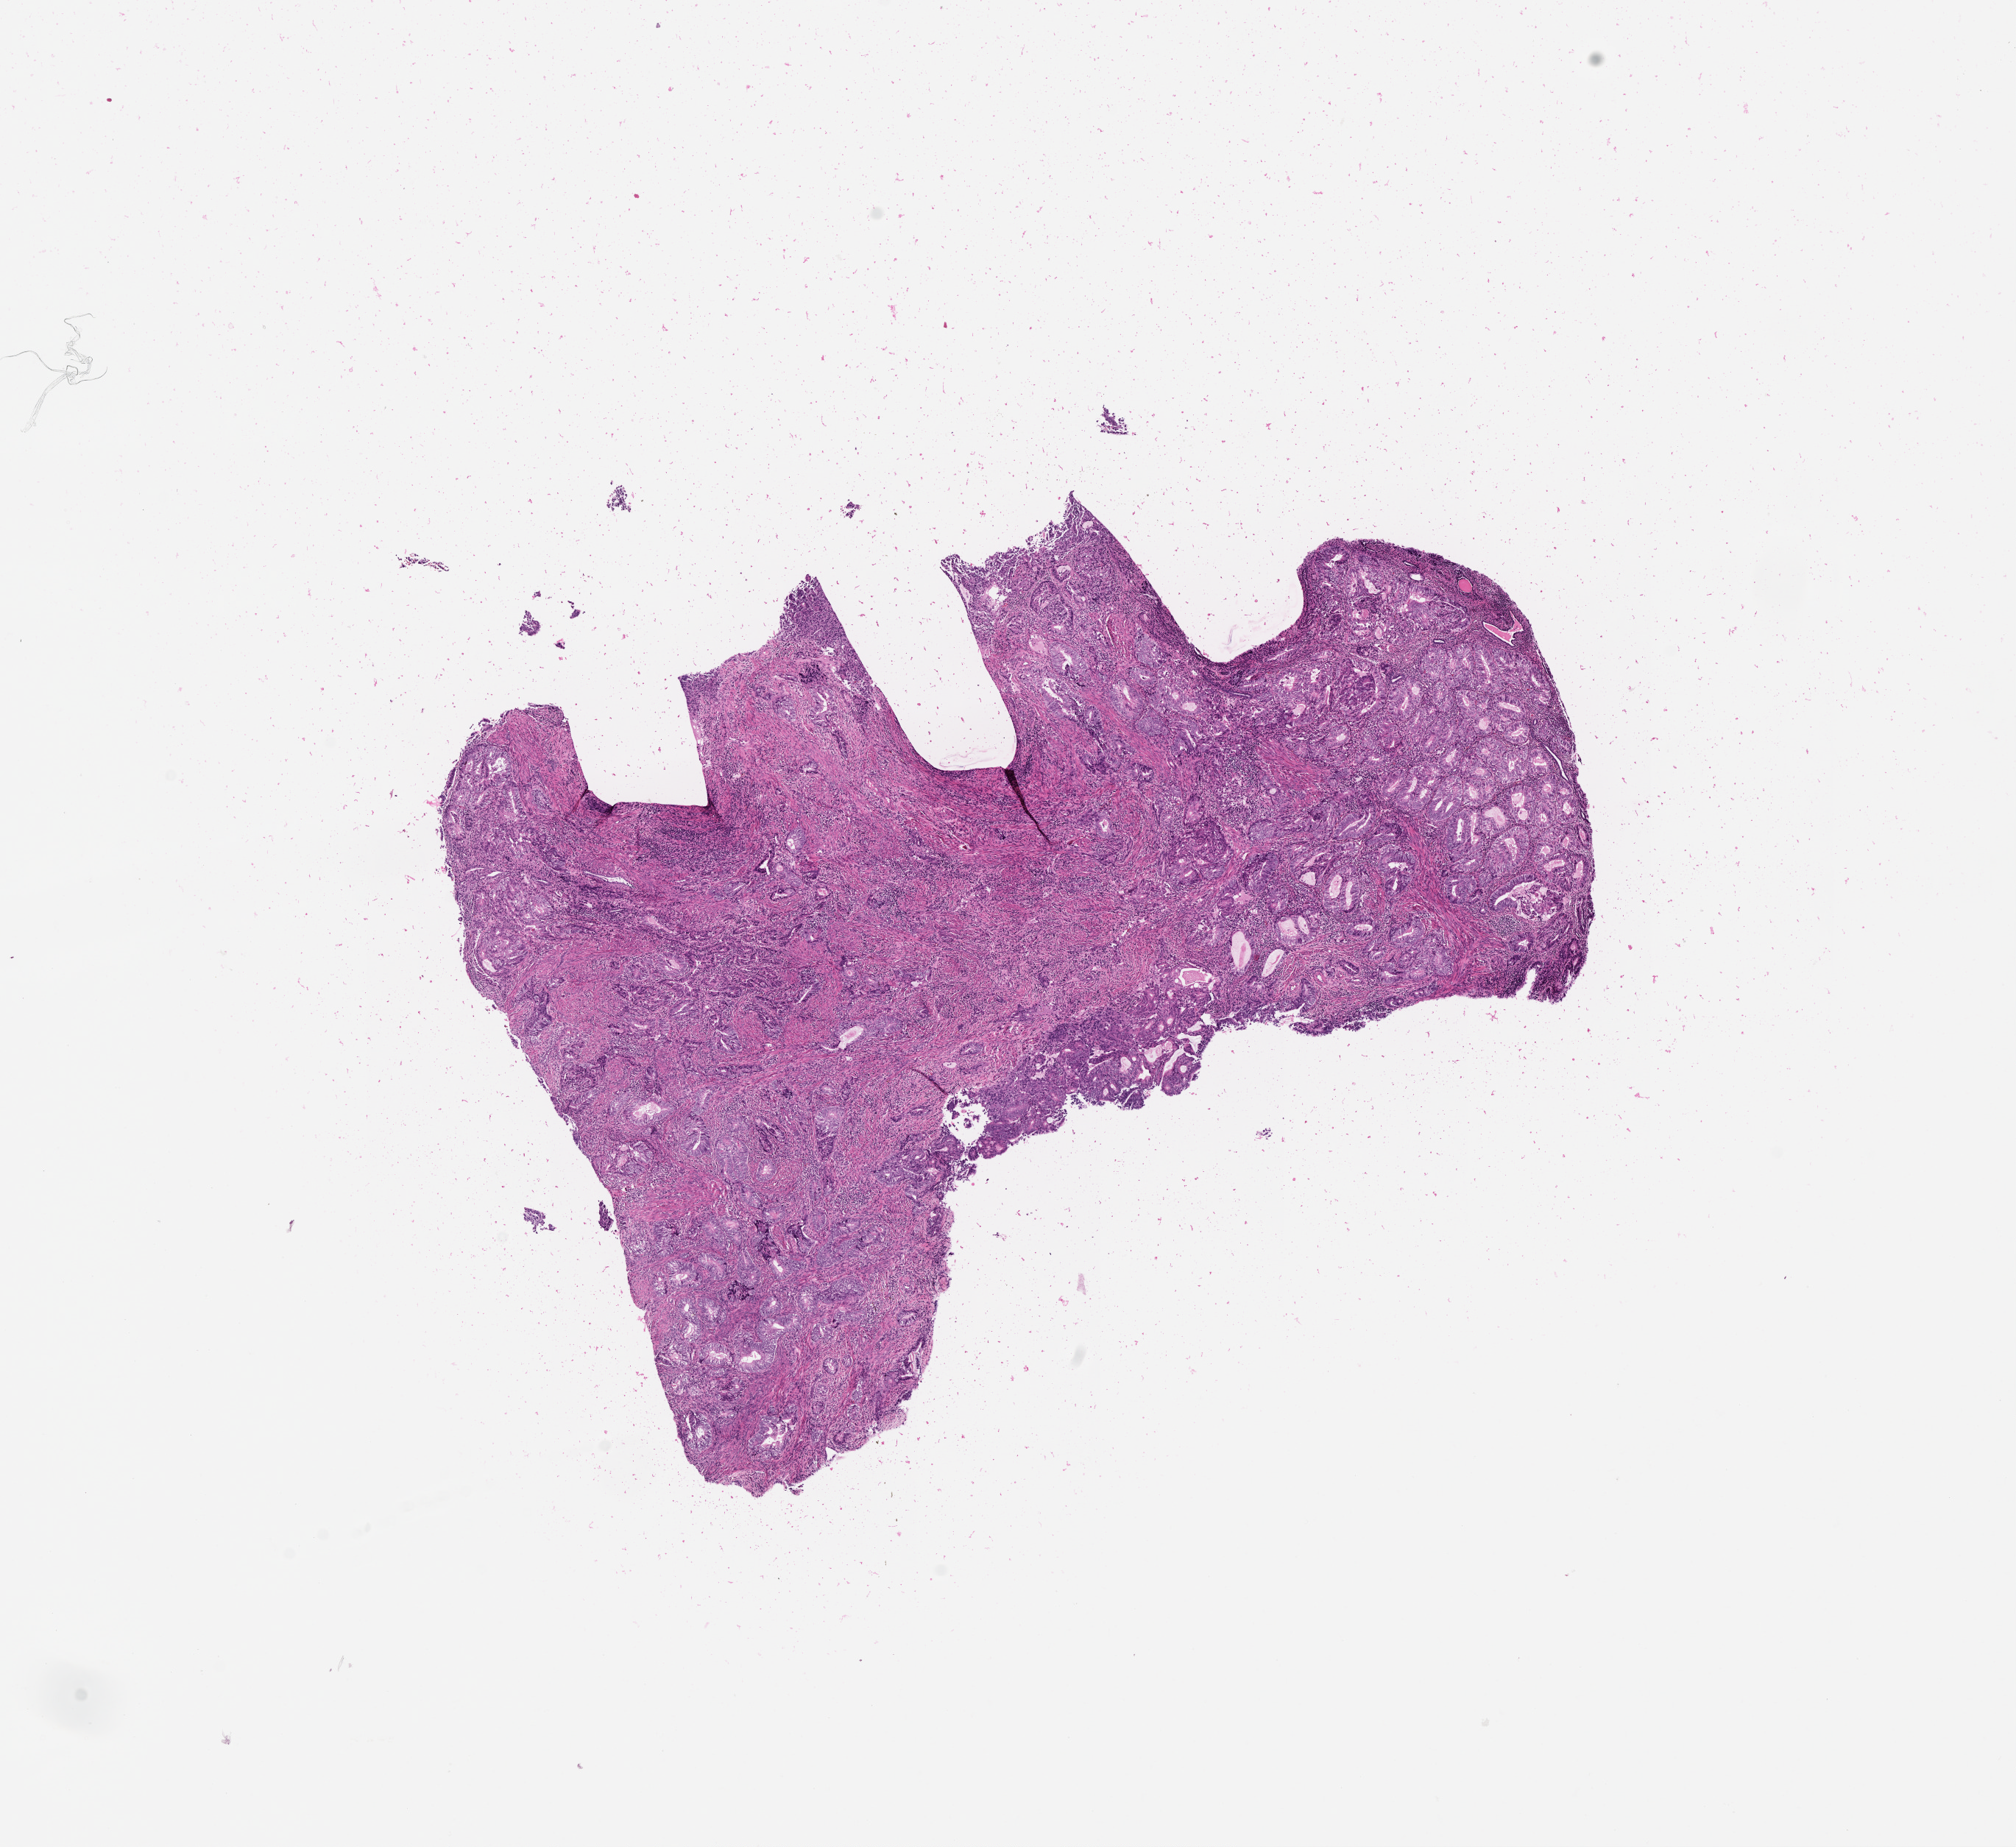
Digitized H&E-stained tissue section (whole slide) — whole scanned area (about 11.0 x 10.1 mm, from a 20x scan) shown as a low-resolution overview; tumour tissue sample, sampled site: uterus. 68-year-old female patient.
Diagnosis: Endometrioid adenocarcinoma, NOS.